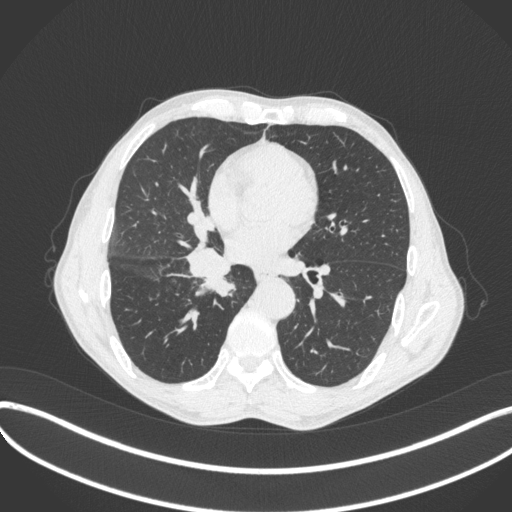
Chest CT, one axial slice; slice 202 of 481 in the series (ordered by position); 120 kVp; lung window (W 1500 / L -600 HU); 1 mm slice thickness; 512 × 512 image matrix. Patient: male, 65 years. From the clinical record (not read from this slice): clinical TNM (as recorded): T2a N0 M0; histopathological grade: G2.
Annotated regions visible in this slice (bounding box drawn by a radiologist):
- lung tumour (recorded histology: squamous cell carcinoma): bounding box (x1, y1, x2, y2) in pixels: (183, 241, 238, 301)